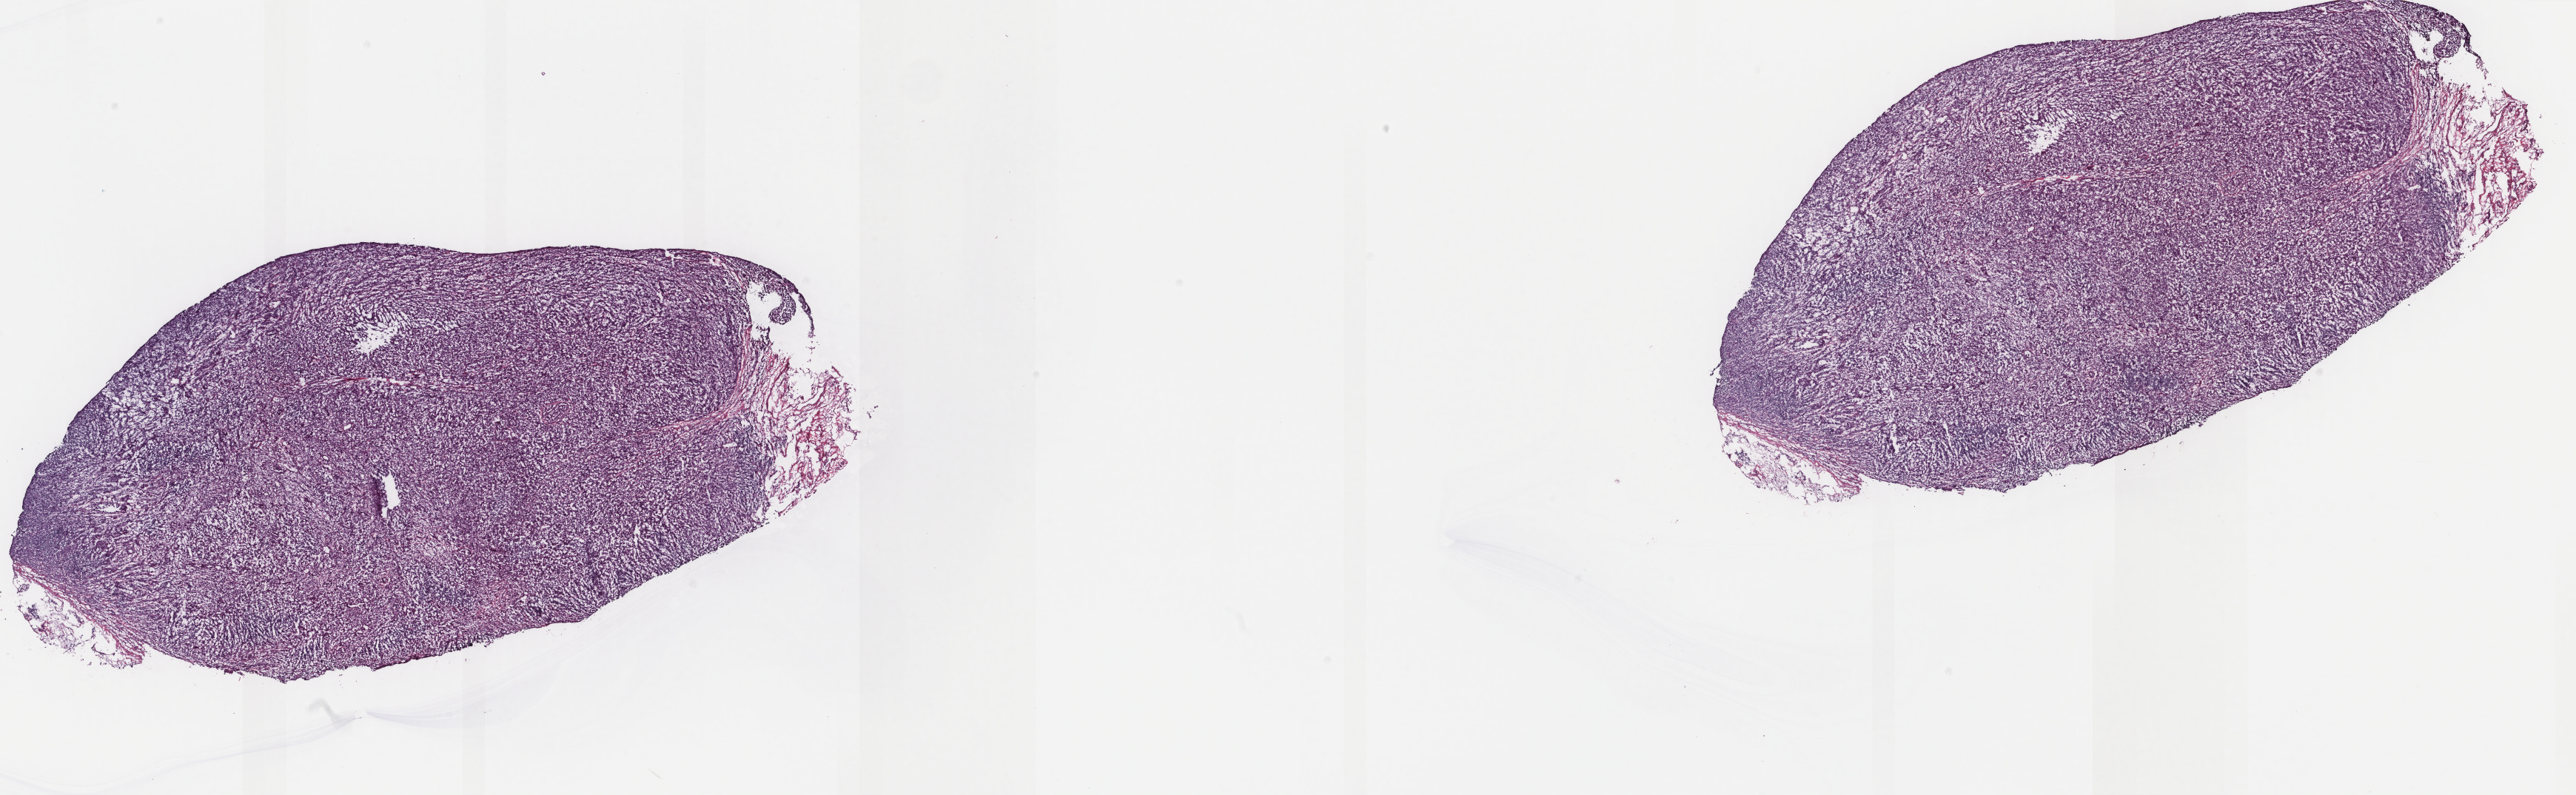
Digitized H&E-stained tissue section (whole slide), a low-resolution overview of the entire scanned area, about 27.6 x 8.5 mm, frozen section from the top of the tissue portion, metastatic tumour sample, sampled site: lymph node. Male patient; age at initial diagnosis 64 years. Pathologist review of this section (percent, as recorded): tumour cells 95%, tumour nuclei 95%, normal cells 5%, stromal cells 0%, necrosis 0%. Infiltration values recorded for this section: lymphocyte infiltration 1%, monocyte infiltration 1%, neutrophil infiltration 0%.
This section: metastatic tumour tissue. Patient diagnosis: Malignant melanoma, NOS.